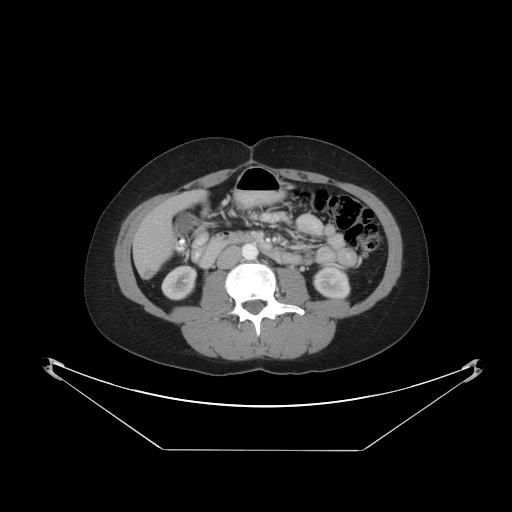
Contrast-enhanced abdominal CT, one axial slice. Slice 13 of 48 in the series (ordered by position). 120 kVp. Intravenous contrast given. Soft-tissue window (W 400 / L 40 HU). 512 × 512 image matrix, field of view 482 × 482 mm. Female patient, age 38 years. From the clinical record (not read from this slice): diagnosis: colorectal cancer liver metastases, imaged before liver resection.
Annotated regions visible in this slice (manually delineated by an expert):
- liver: bounding box [x1, y1, x2, y2] px = [135, 193, 203, 279]
- planned liver remnant (the part of the liver to remain after resection): [170, 193, 202, 209]
- liver metastasis: [146, 271, 154, 276]